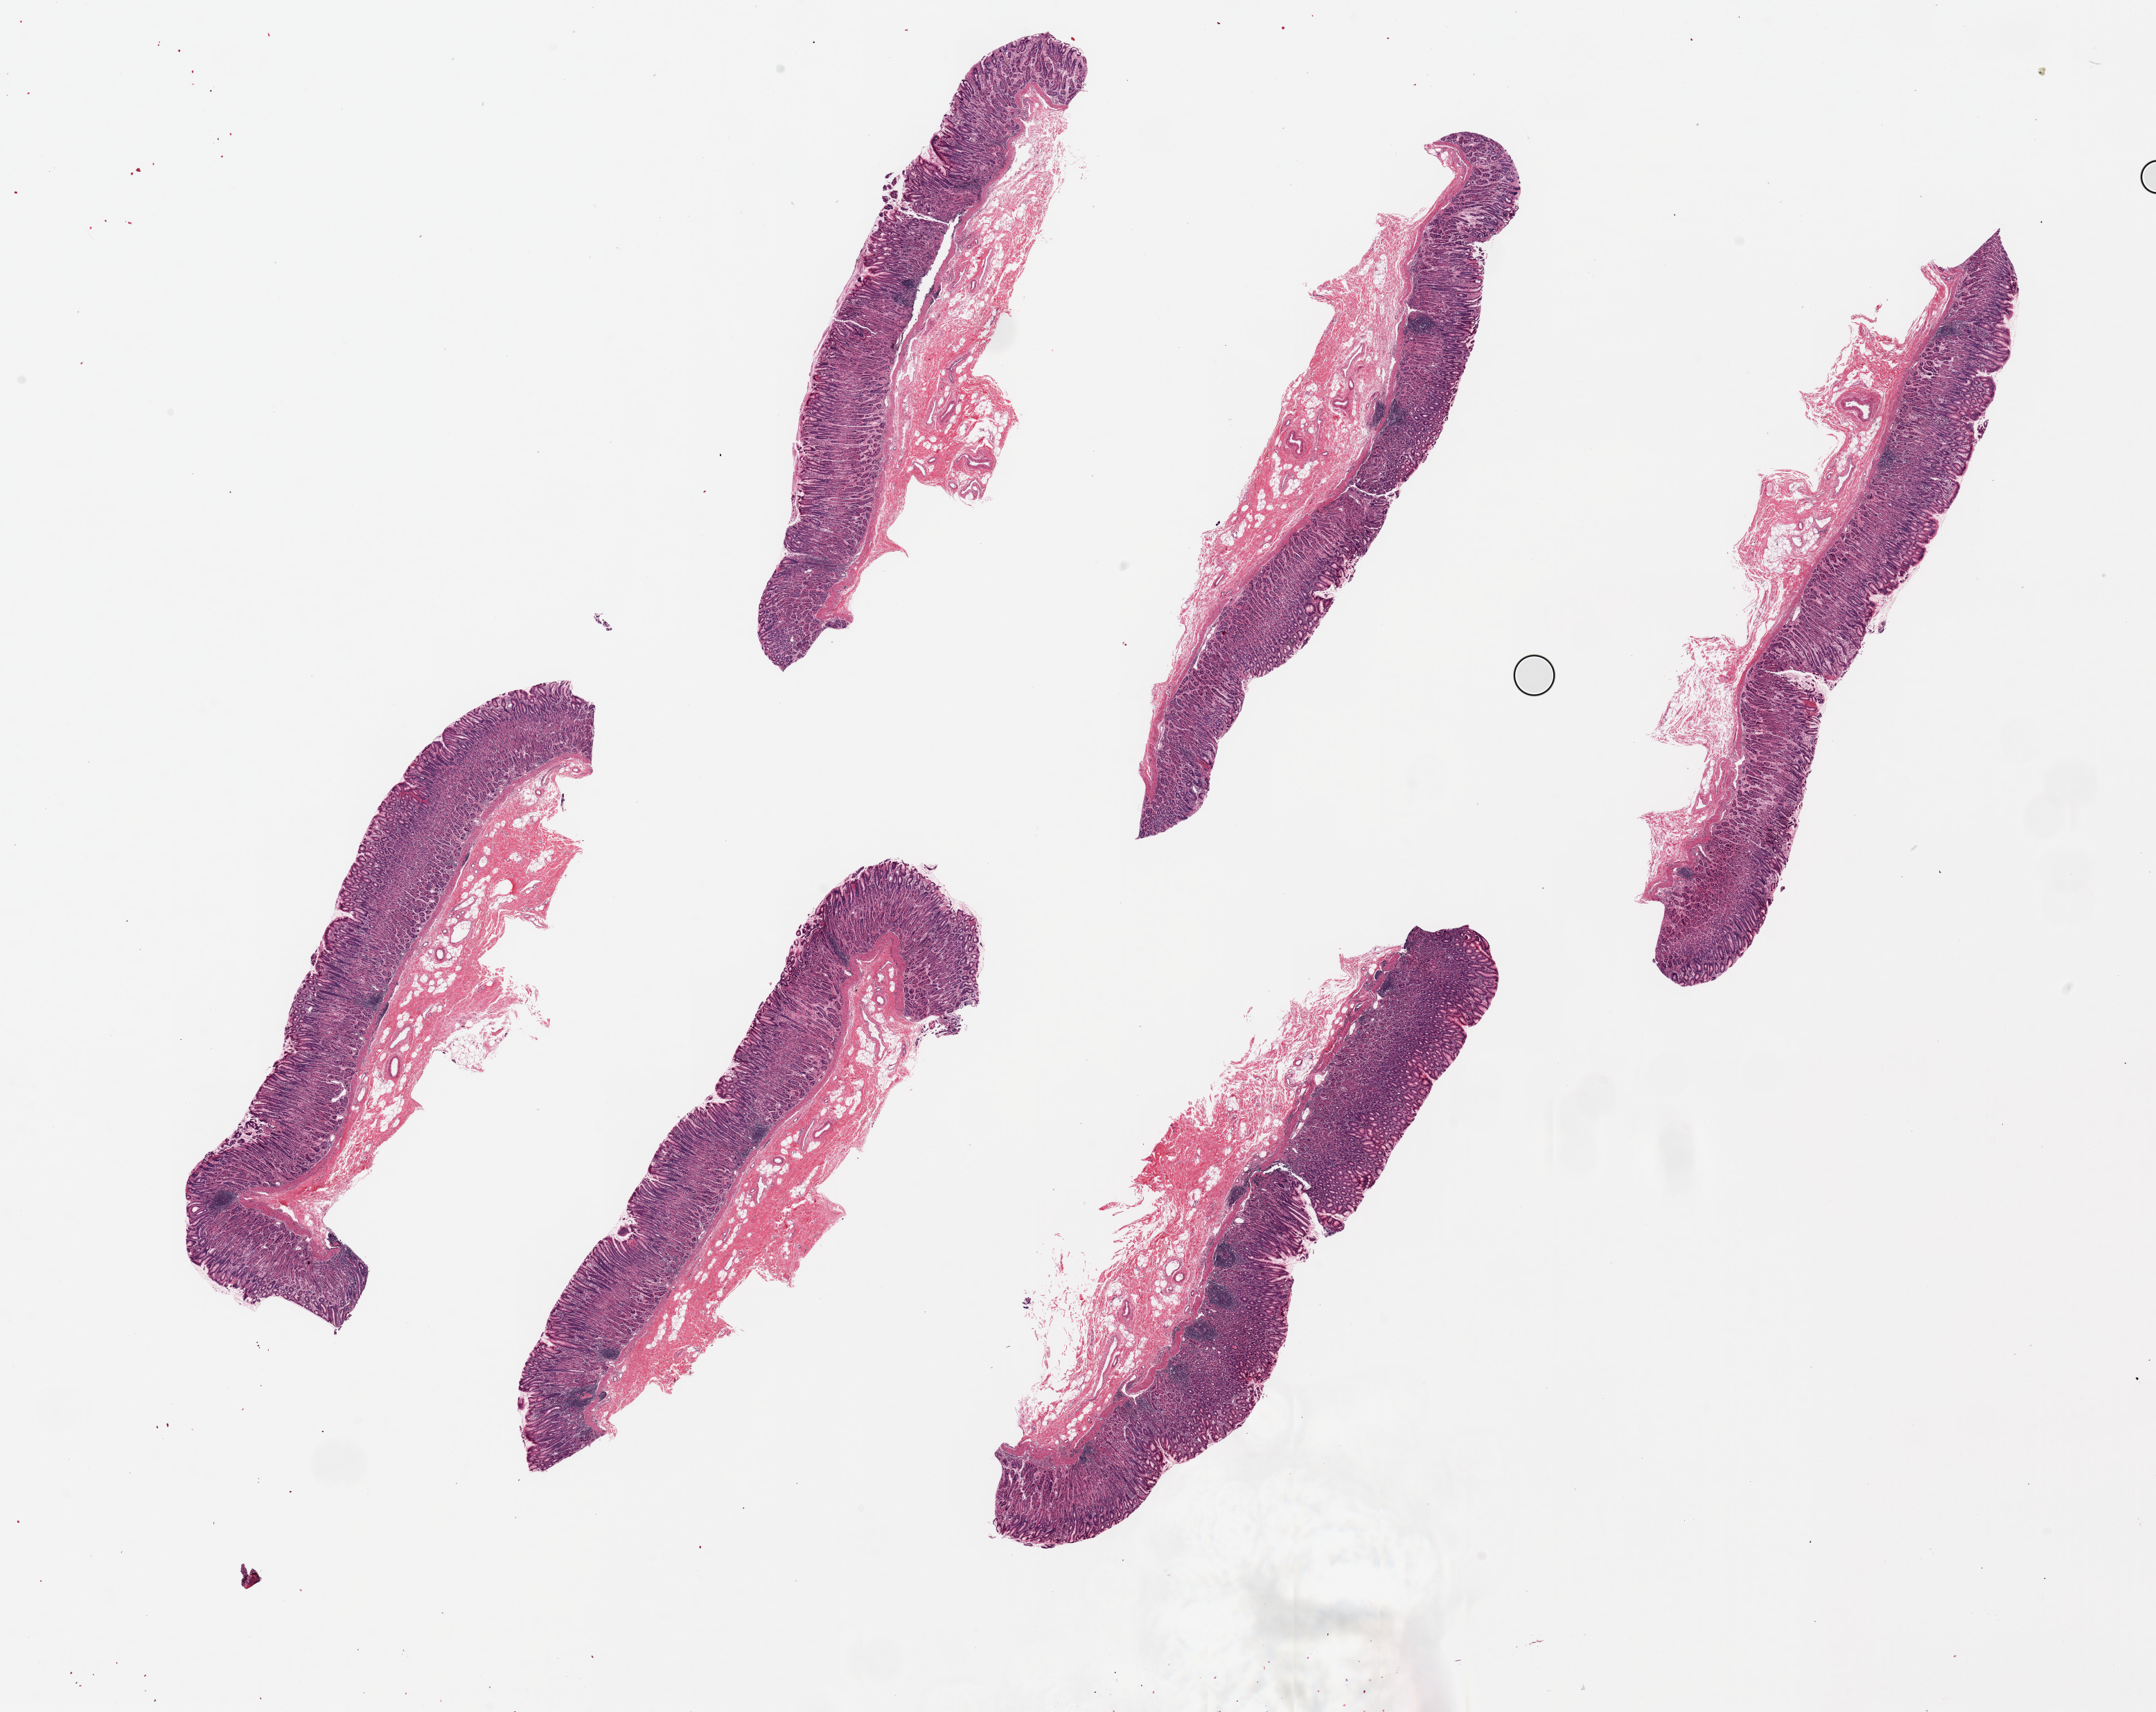
Haematoxylin and eosin whole-slide image, brightfield, a low-resolution overview of the entire scanned area, about 24.6 x 19.5 mm. PAXgene-fixed, paraffin-embedded tissue. Sampled site (target tissue): stomach. Donor tissue sample.
Pathologist's review note for this sample: 6 pieces, ~9x1.5mm, remarkably well-preserved mucosa 50-70% of thickness.